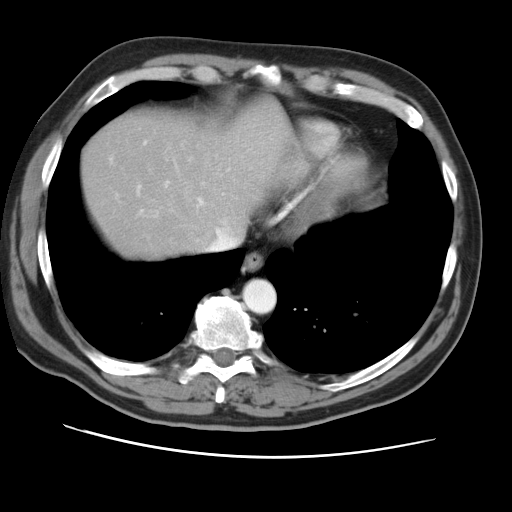
Contrast-enhanced abdominal CT, one axial slice; slice 43 of 49 in the series (ordered by position); intravenous contrast given; soft-tissue window (W 400 / L 40 HU); 5 mm slice thickness; 512 × 512 image matrix, field of view 374 × 374 mm. Male patient, age 59 years. From the clinical record (not read from this slice): diagnosis: colorectal cancer liver metastases, imaged before liver resection.
Outlined on this slice (outlined manually by an expert reader):
- hepatic veins: box from (x=195, y=220) to (x=239, y=251) px
- liver: (x=82, y=102)–(x=284, y=258)
- planned liver remnant (the part of the liver to remain after resection): (x=82, y=103)–(x=284, y=258)
- portal vein (with intrahepatic branches): (x=109, y=156)–(x=202, y=212)